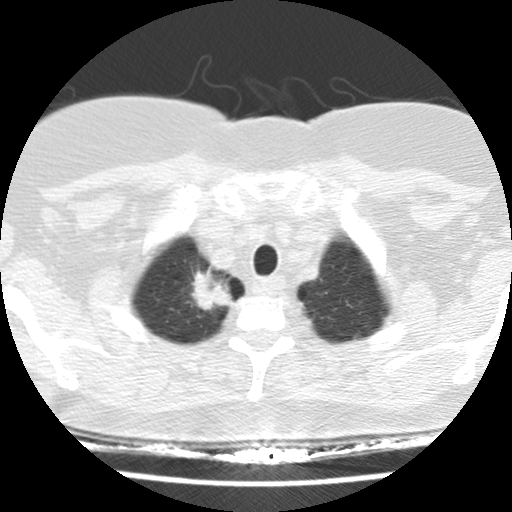
Chest CT (low-dose screening protocol), one axial image; first (baseline) screen; lung window (W 1500 / L -600 HU); 512 × 512 image matrix. Female, age 58 years at enrolment. Former smoker at enrolment.
Expert-annotated lung lesion, box from (x=168, y=254) to (x=246, y=331) px. The exam's reader record, not a measurement of the box and not confirmed to be the same lesion: non-calcified nodule or mass ≥4 mm, right upper lobe, 28 × 24 mm, spiculated (stellate) margins, soft tissue attenuation. Lung cancer was diagnosed 40 days after this screen: adenocarcinoma, NOS, right upper lobe, poorly differentiated (G3), stage IB (AJCC 6th edition), 29 mm at pathology.